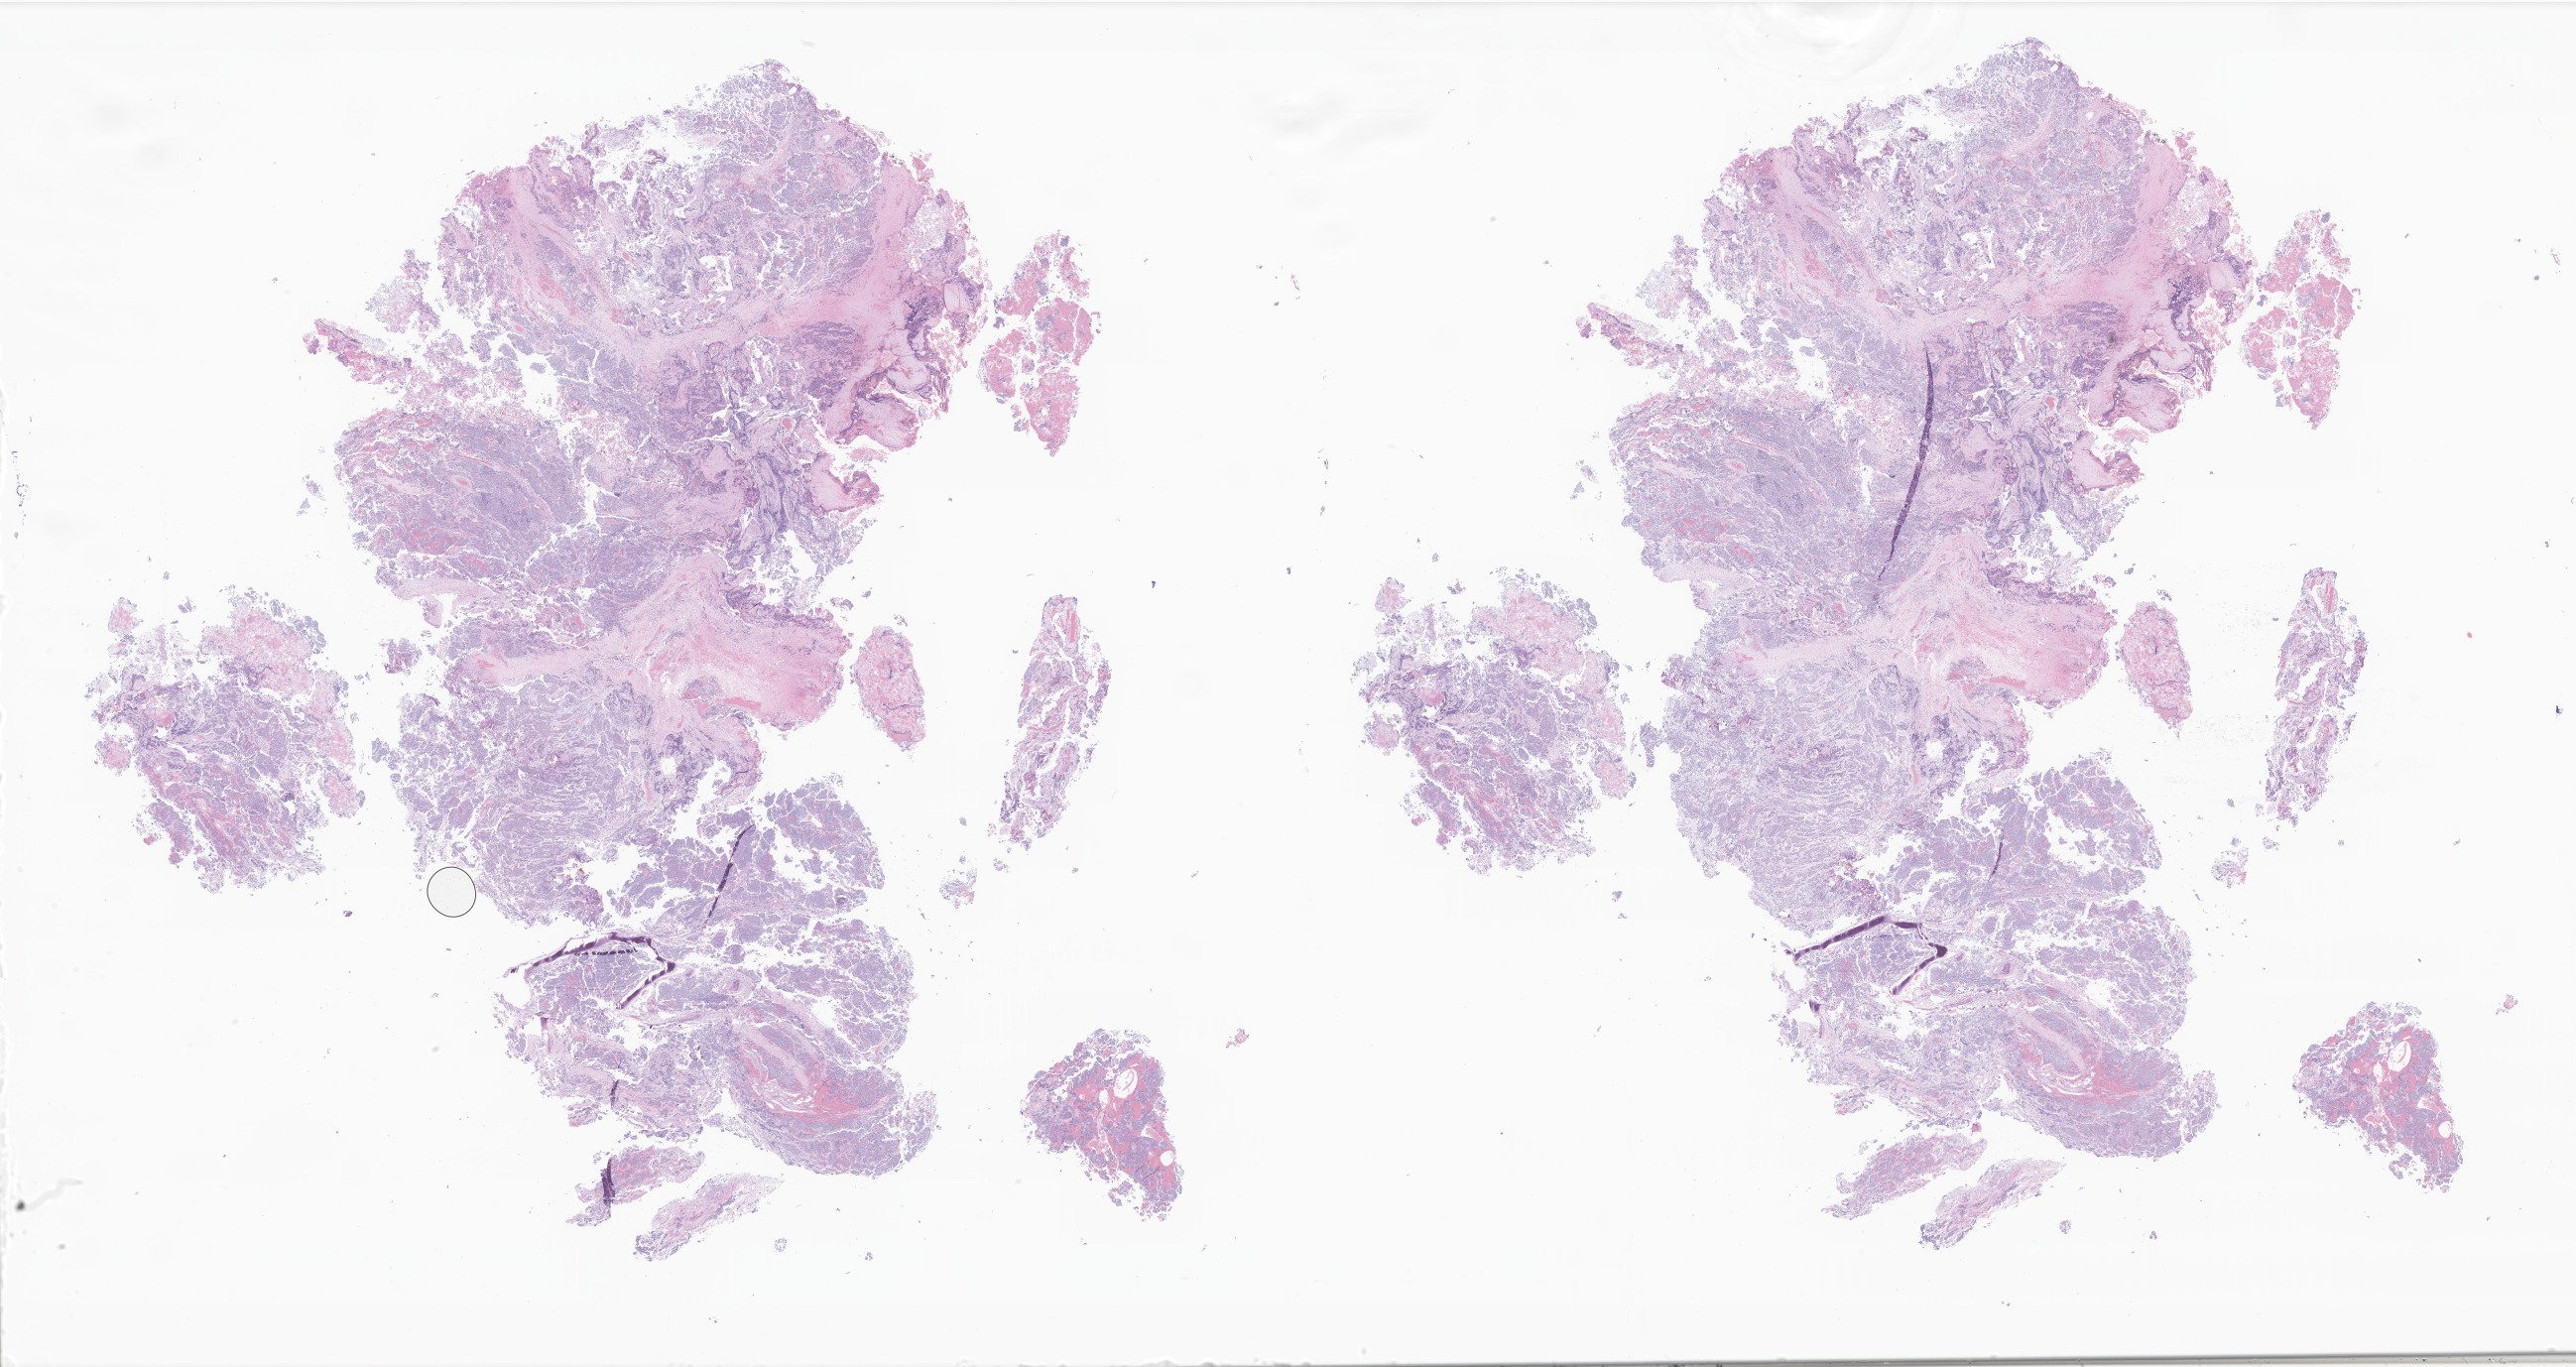
H&E whole-slide image of tumor tissue from the brain — whole scanned area (about 43.8 x 23.2 mm) shown as a low-resolution overview; FFPE section. Patient: male, age 609 days (about 1.7 years).
* diagnosis (ICD-O-3 morphology term): Neuroblastoma, NOS